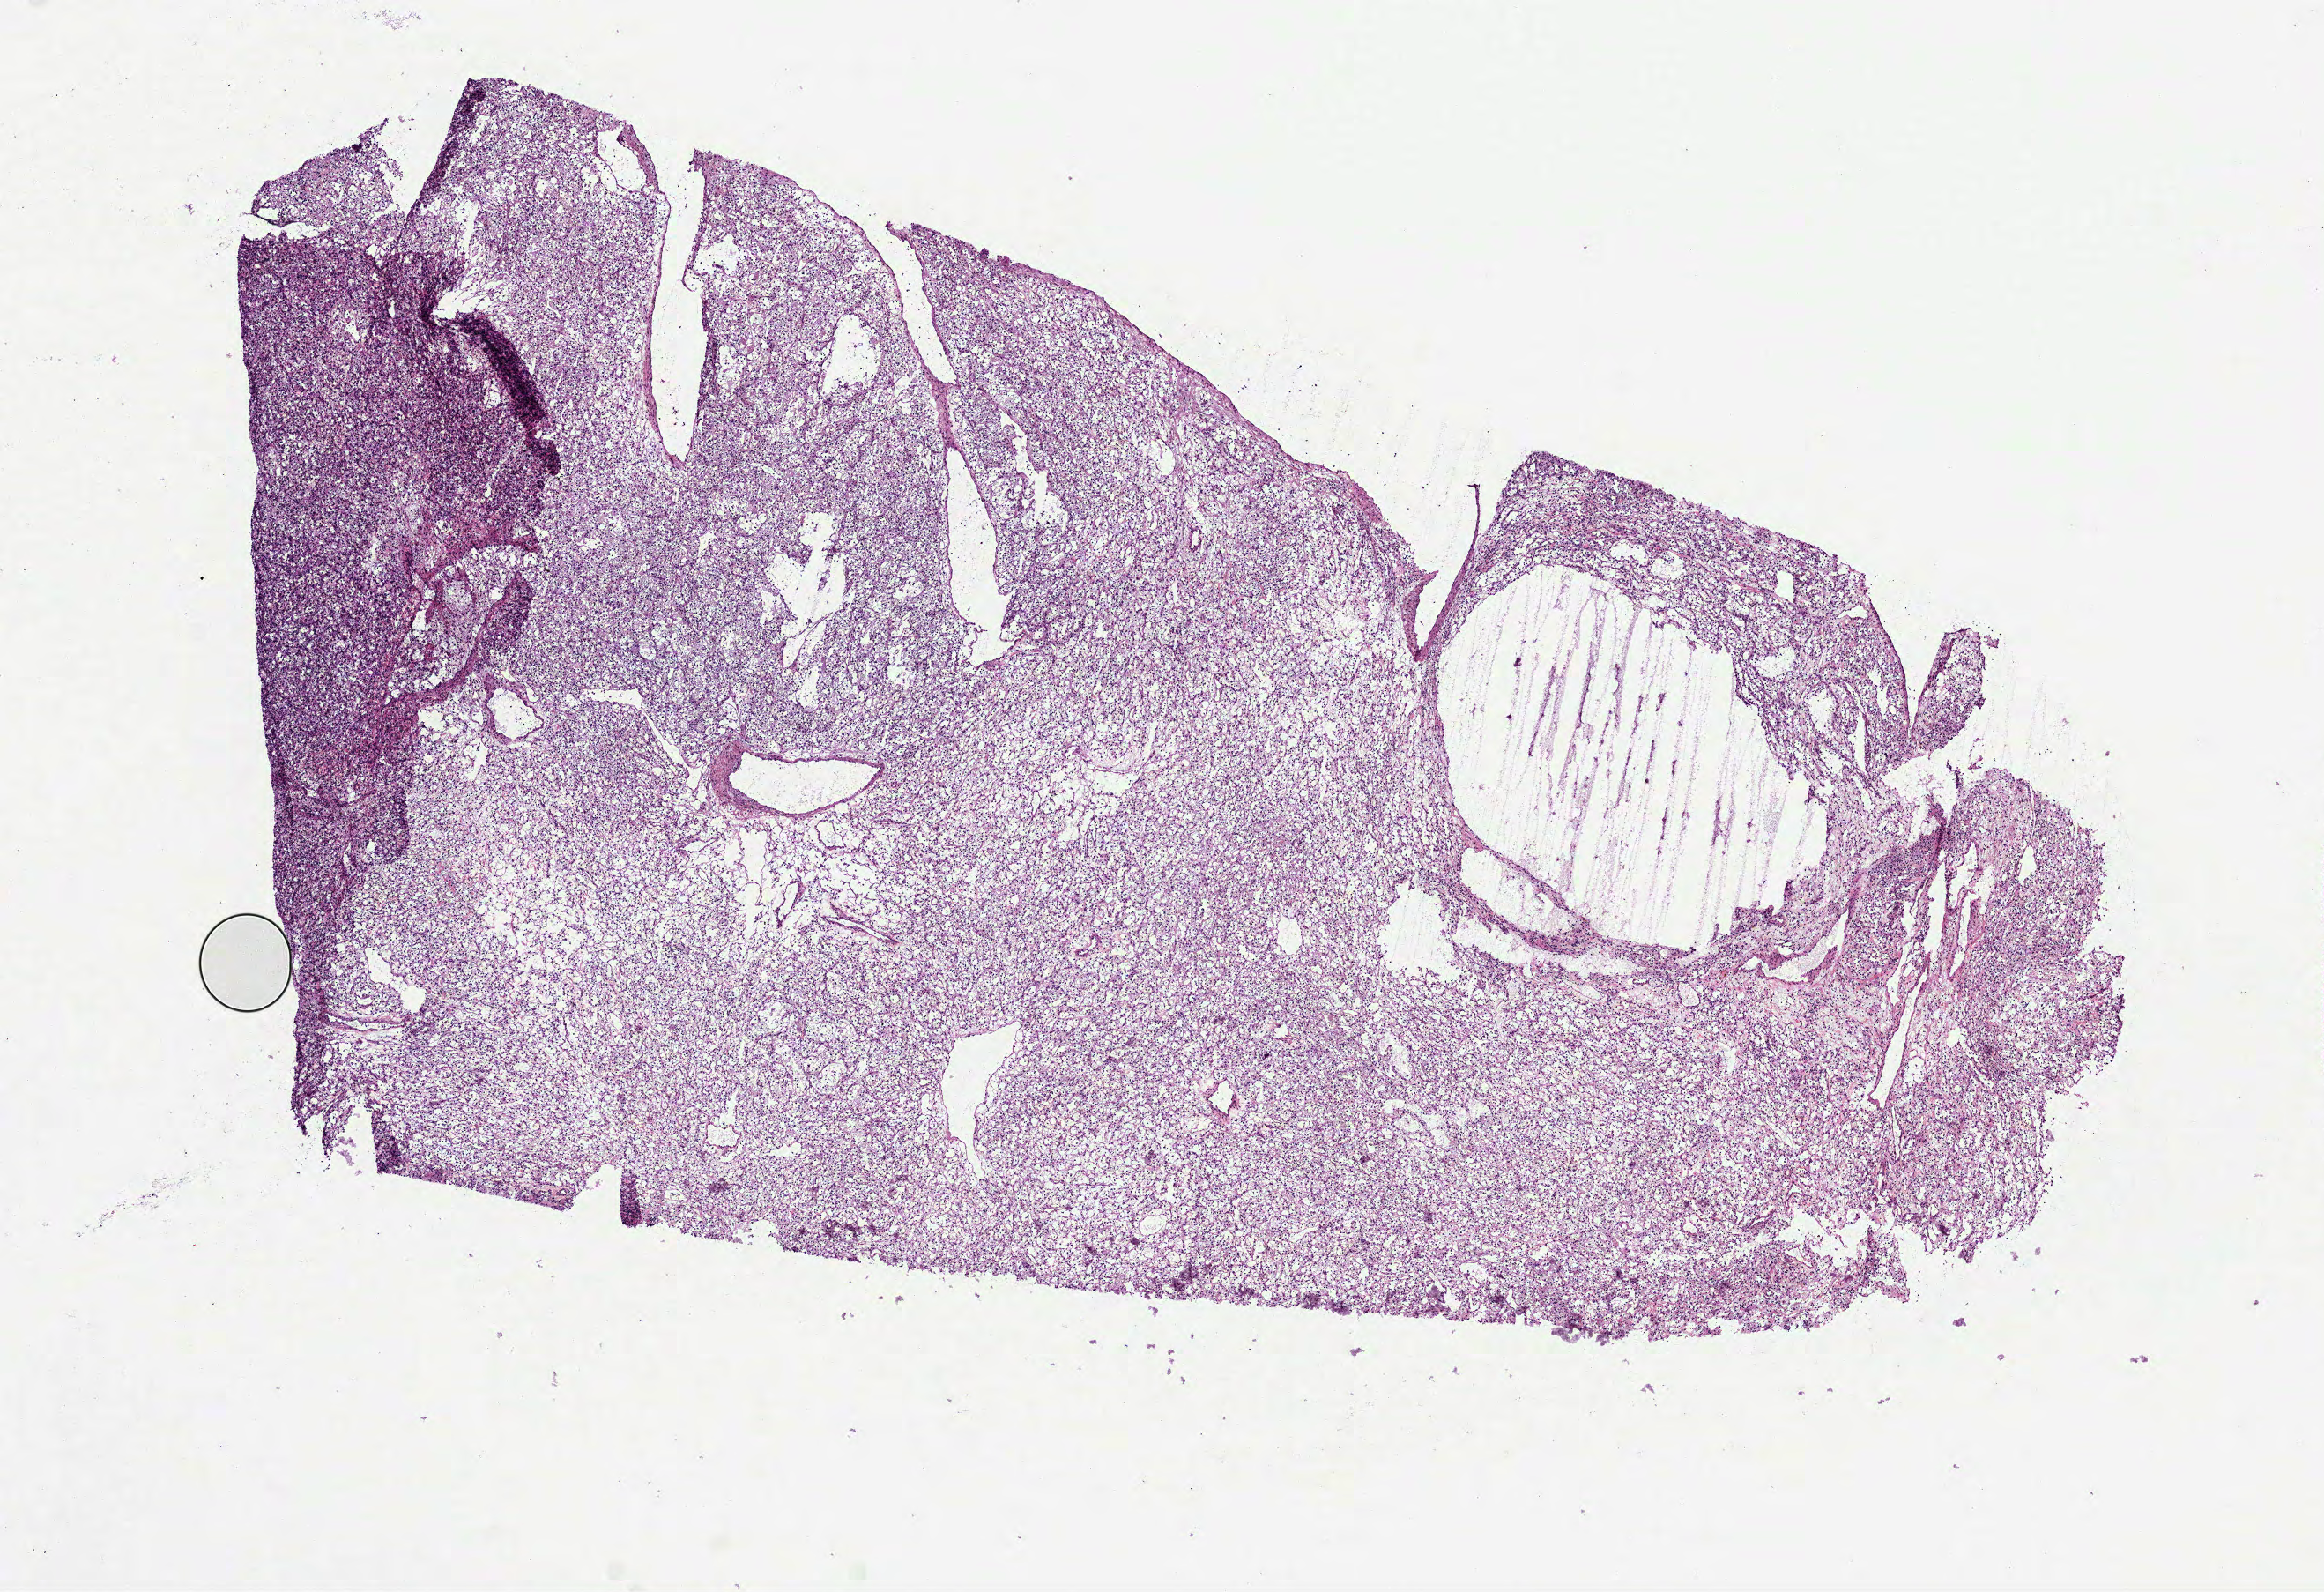
Digitized Hematoxylin and eosin (H&E) stained tissue section (whole slide) — low-resolution overview of the scanned area, about 10.6 x 7.3 mm, frozen section from the top of the tissue portion, kidney, primary tumour sample. Patient: male, age at initial diagnosis 55 years.
Histologic diagnosis: Clear cell adenocarcinoma, NOS.